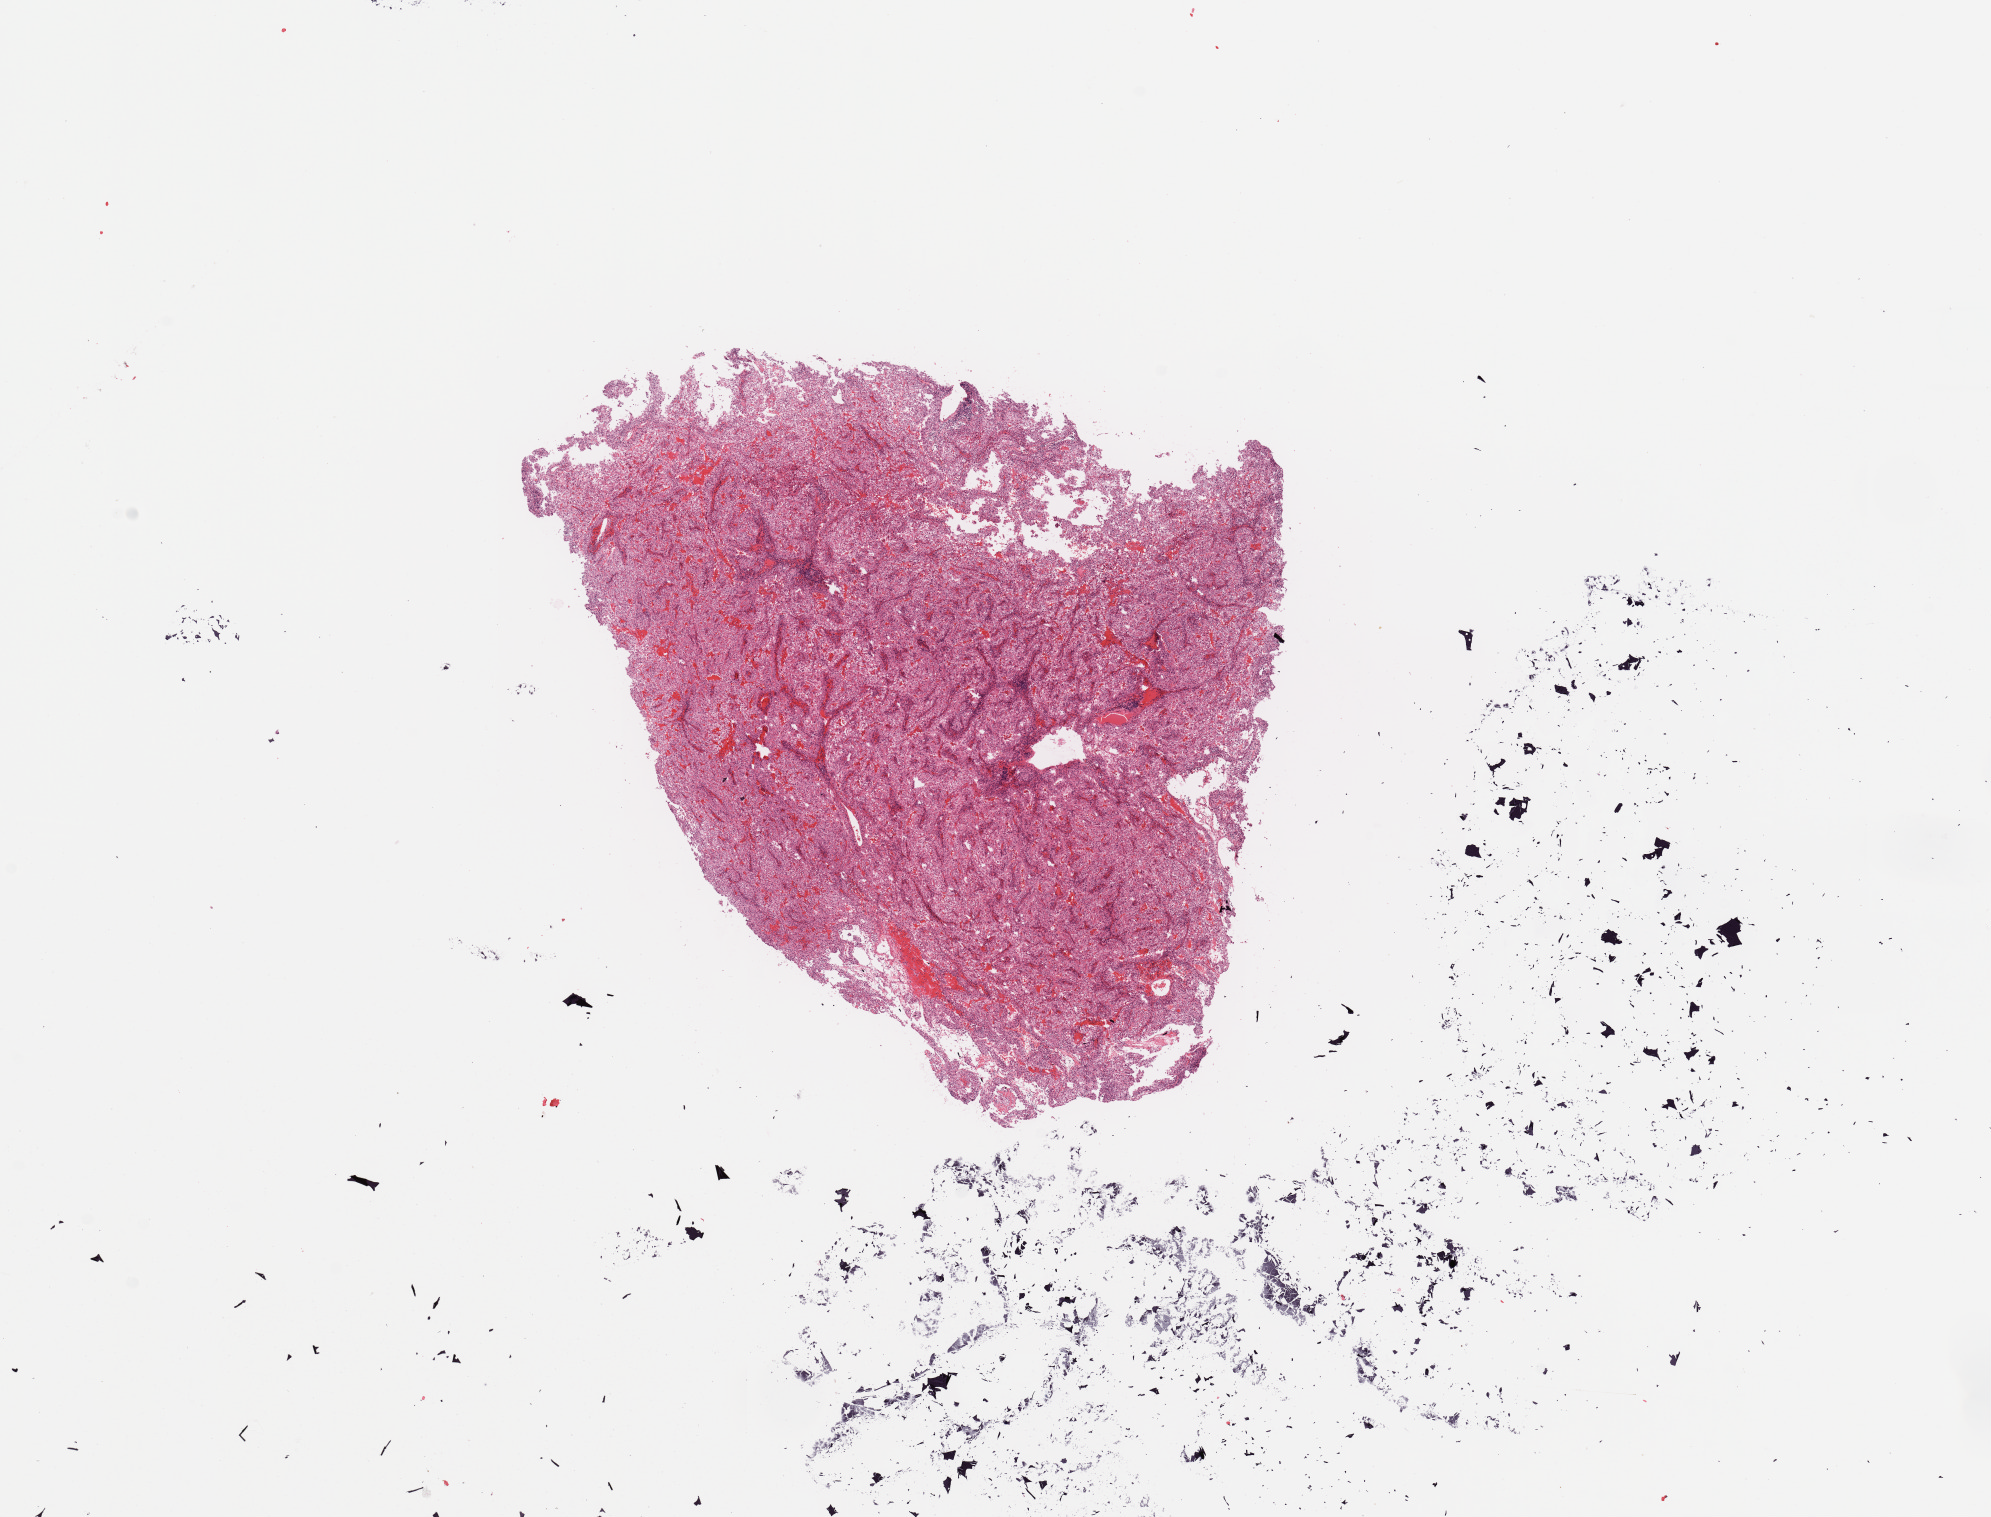
Hematoxylin and eosin (H&E) stained whole-slide image, whole scanned area (about 15.8 x 12.0 mm, slide scanned at 20x) shown as a low-resolution overview, tumour tissue sample, sampled site: kidney. Patient: male, age 41 years. Histologic grade: G3 (poorly differentiated). Slide review estimates, as recorded: tumour nuclei 80%, necrosis 0%.
AJCC pathologic stage: I. Diagnosis: Renal cell carcinoma, NOS.